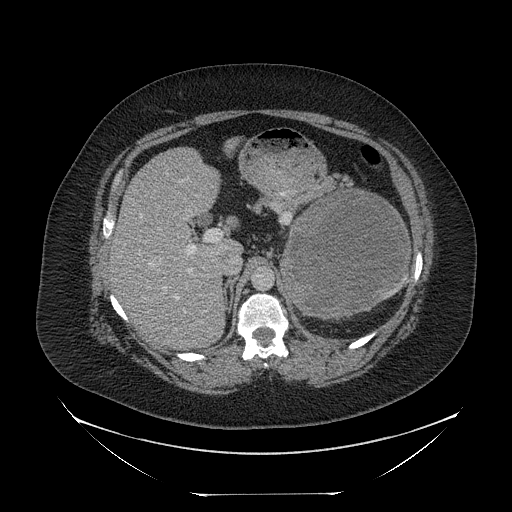
Contrast-enhanced abdominal CT, one axial slice. Position 152 of 205 along the scan axis. Reconstruction kernel STANDARD. 120 kVp. Intravenous contrast given. Soft-tissue window (W 400 / L 40 HU). 512 × 512 image matrix, field of view 500 × 500 mm. Patient: female, 53 years. Case-level facts recorded for this patient, not image findings: diagnosis: adrenocortical carcinoma; tumour side: left adrenal; tumour size at pathology: 17 cm; Ki-67 index: 20 %; stage (as recorded): 3.
Outlined on this slice (semi-automatically segmented with operator editing):
- mass: bounding box <286,191,409,318> (left, top, right, bottom; pixels)